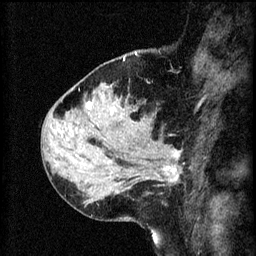
Breast MRI (dynamic contrast-enhanced), one sagittal slice. 3 images stored at this slice position (order not interpretable as contrast timing). 1.5 T. TE 4.2 ms, TR 8.2 ms. 2 mm slice thickness. 256 × 256 image matrix, field of view 180 × 180 mm. Female patient, age 37 years.
Outlined on this slice (semi-automatic segmentation, software-assisted and operator-edited):
- analysis volume of interest (the breast-tissue region the enhancement analysis was run in; not a lesion): bounding box <124,138,183,195> (left, top, right, bottom; pixels)
- tumour enhancement mask (voxels above the 70 % enhancement threshold inside the analysis volume of interest): <147,150,181,183>